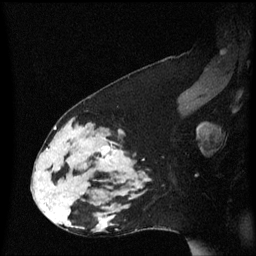
Breast MRI (dynamic contrast-enhanced), one sagittal slice; slice 37 of 60 in the series (ordered by position); dynamic contrast-enhanced series, image 2 of 3 at this slice position (ordered by acquisition); 1.5 T; TE 4.2 ms, TR 8.4 ms; 2 mm slice thickness; 256 × 256 image matrix, field of view 210 × 210 mm. Female patient, age 33 years. Case-level facts recorded for this patient, not image findings: setting: breast cancer imaged before/during neoadjuvant chemotherapy; receptor status: triple-negative.
Structures marked on this image (semi-automatically segmented with operator editing):
- analysis volume of interest (the breast-tissue region the enhancement analysis was run in; not a lesion): box from (x=44, y=123) to (x=139, y=189) px
- tumour enhancement mask (voxels above the 70 % enhancement threshold inside the analysis volume of interest): (x=58, y=139)–(x=119, y=170)